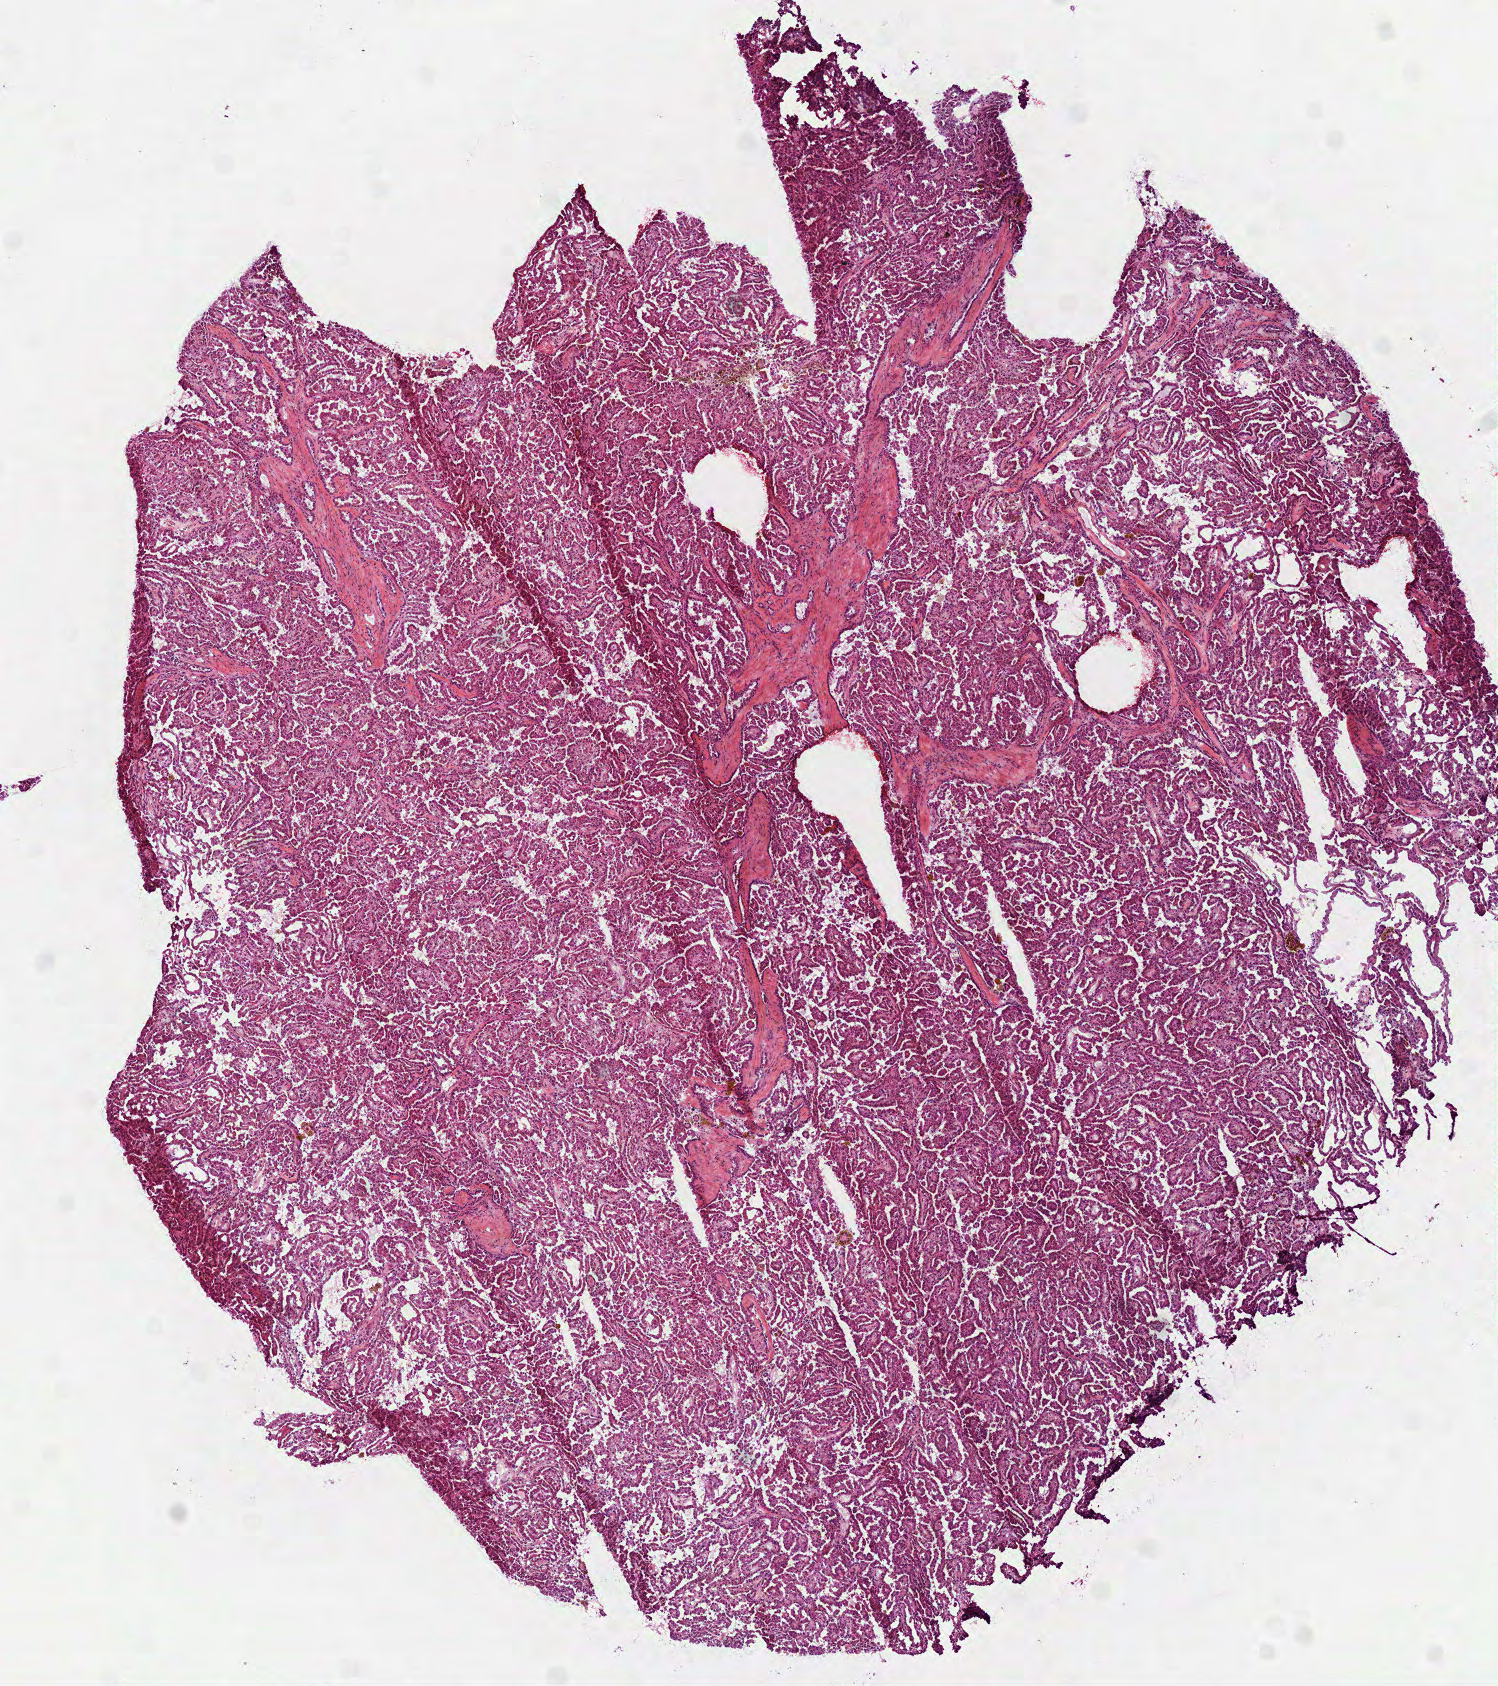
Whole-slide histology image, H&E-stained — a low-resolution overview of the entire scanned area, about 6.0 x 6.8 mm (acquisition: 40x scan). Frozen section from the top of the tissue portion. Kidney, primary tumour sample. Female, age 71 years at initial diagnosis.
Diagnosis: Papillary adenocarcinoma, NOS.